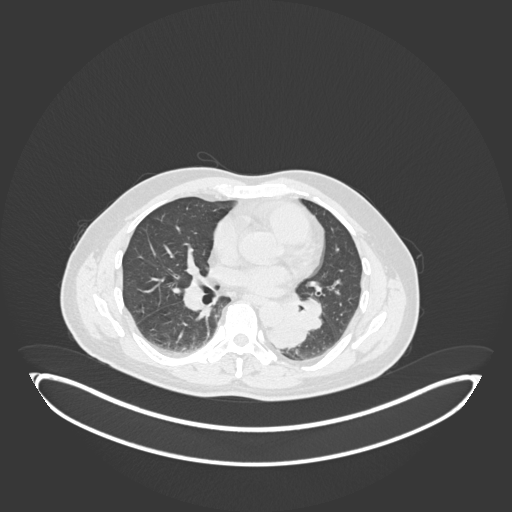
Chest CT, one axial slice. Slice 95 of 258 in the series (ordered by position). 120 kVp. Lung window (W 1500 / L -600 HU). 512 × 512 image matrix, field of view 500 × 500 mm. Patient: male, 54 years. From the clinical record (not read from this slice): clinical TNM (as recorded): T3 N0 M0.
Outlined on this slice (rectangle marked by the reading radiologist):
- lung tumour (recorded histology: squamous cell carcinoma): bounding box [x1, y1, x2, y2] px = [260, 306, 307, 347]